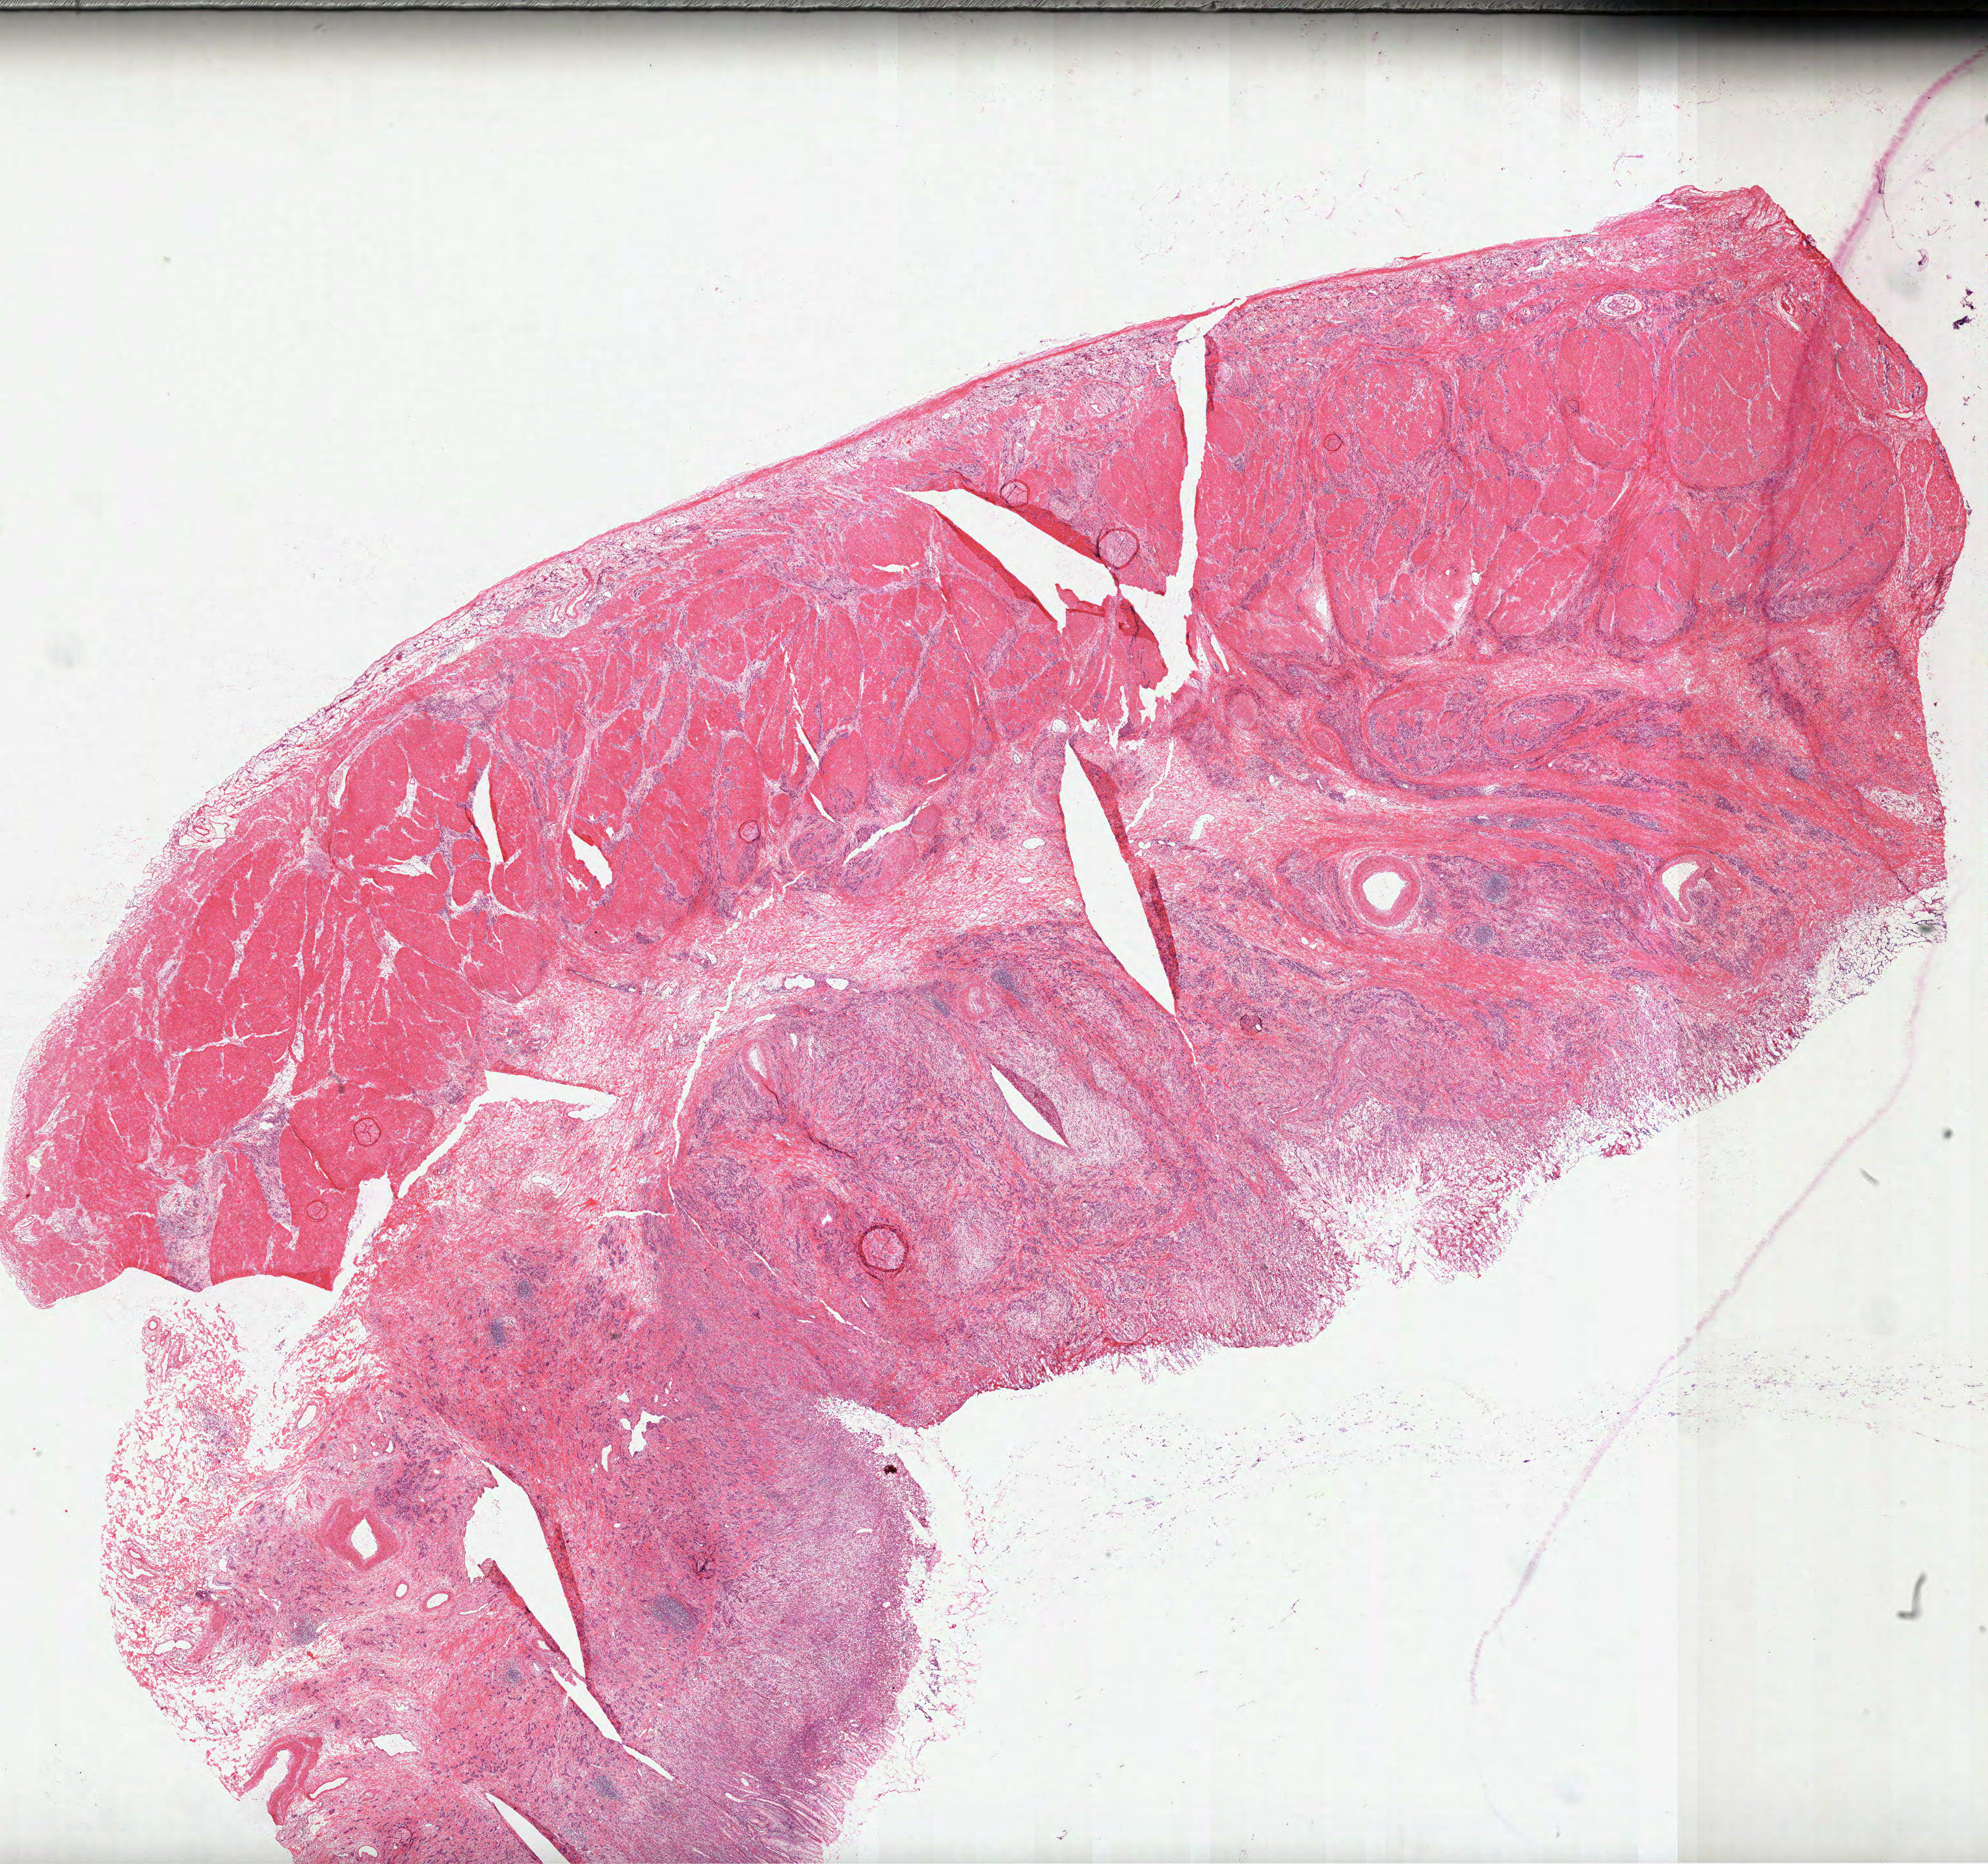
Whole-slide histology image, Hematoxylin and eosin (H&E) stained — low-resolution overview of the scanned area, about 24.7 x 23.1 mm, frozen section from the top of the tissue portion, primary tumour sample from the stomach. Male patient; age at initial diagnosis 55 years. Histologic grade: G3 (poorly differentiated). Slide review estimates, as recorded: tumour cells 100%, tumour nuclei 65%, normal cells 0%, stromal cells 0%, necrosis 0%. Inflammatory infiltration, as recorded: lymphocyte infiltration 10%, monocyte infiltration 0%, neutrophil infiltration 10%.
TNM: T4a N3a M0. AJCC pathologic stage: IIIC. Histologic diagnosis: Adenocarcinoma, NOS (gastric antrum). Lymph nodes positive (case pathology): 11 of 15 examined.